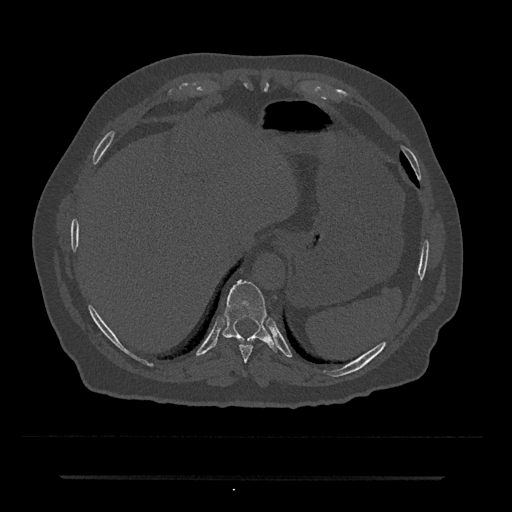
CT including the spine, one axial slice; position 245 of 797 along the scan axis; reconstruction kernel Br40s/3; 120 kVp; bone window (W 1800 / L 400 HU); 0.5 mm slice thickness; 512 × 512 image matrix, field of view 437 × 437 mm. Male patient, age 69 years. From the clinical record (not read from this slice): primary cancer: prostate.
Annotated regions visible in this slice (semi-automatically segmented with operator editing):
- T10 vertebra: box from (x=223, y=280) to (x=277, y=352) px
- T9 vertebra: (x=239, y=345)–(x=253, y=363)